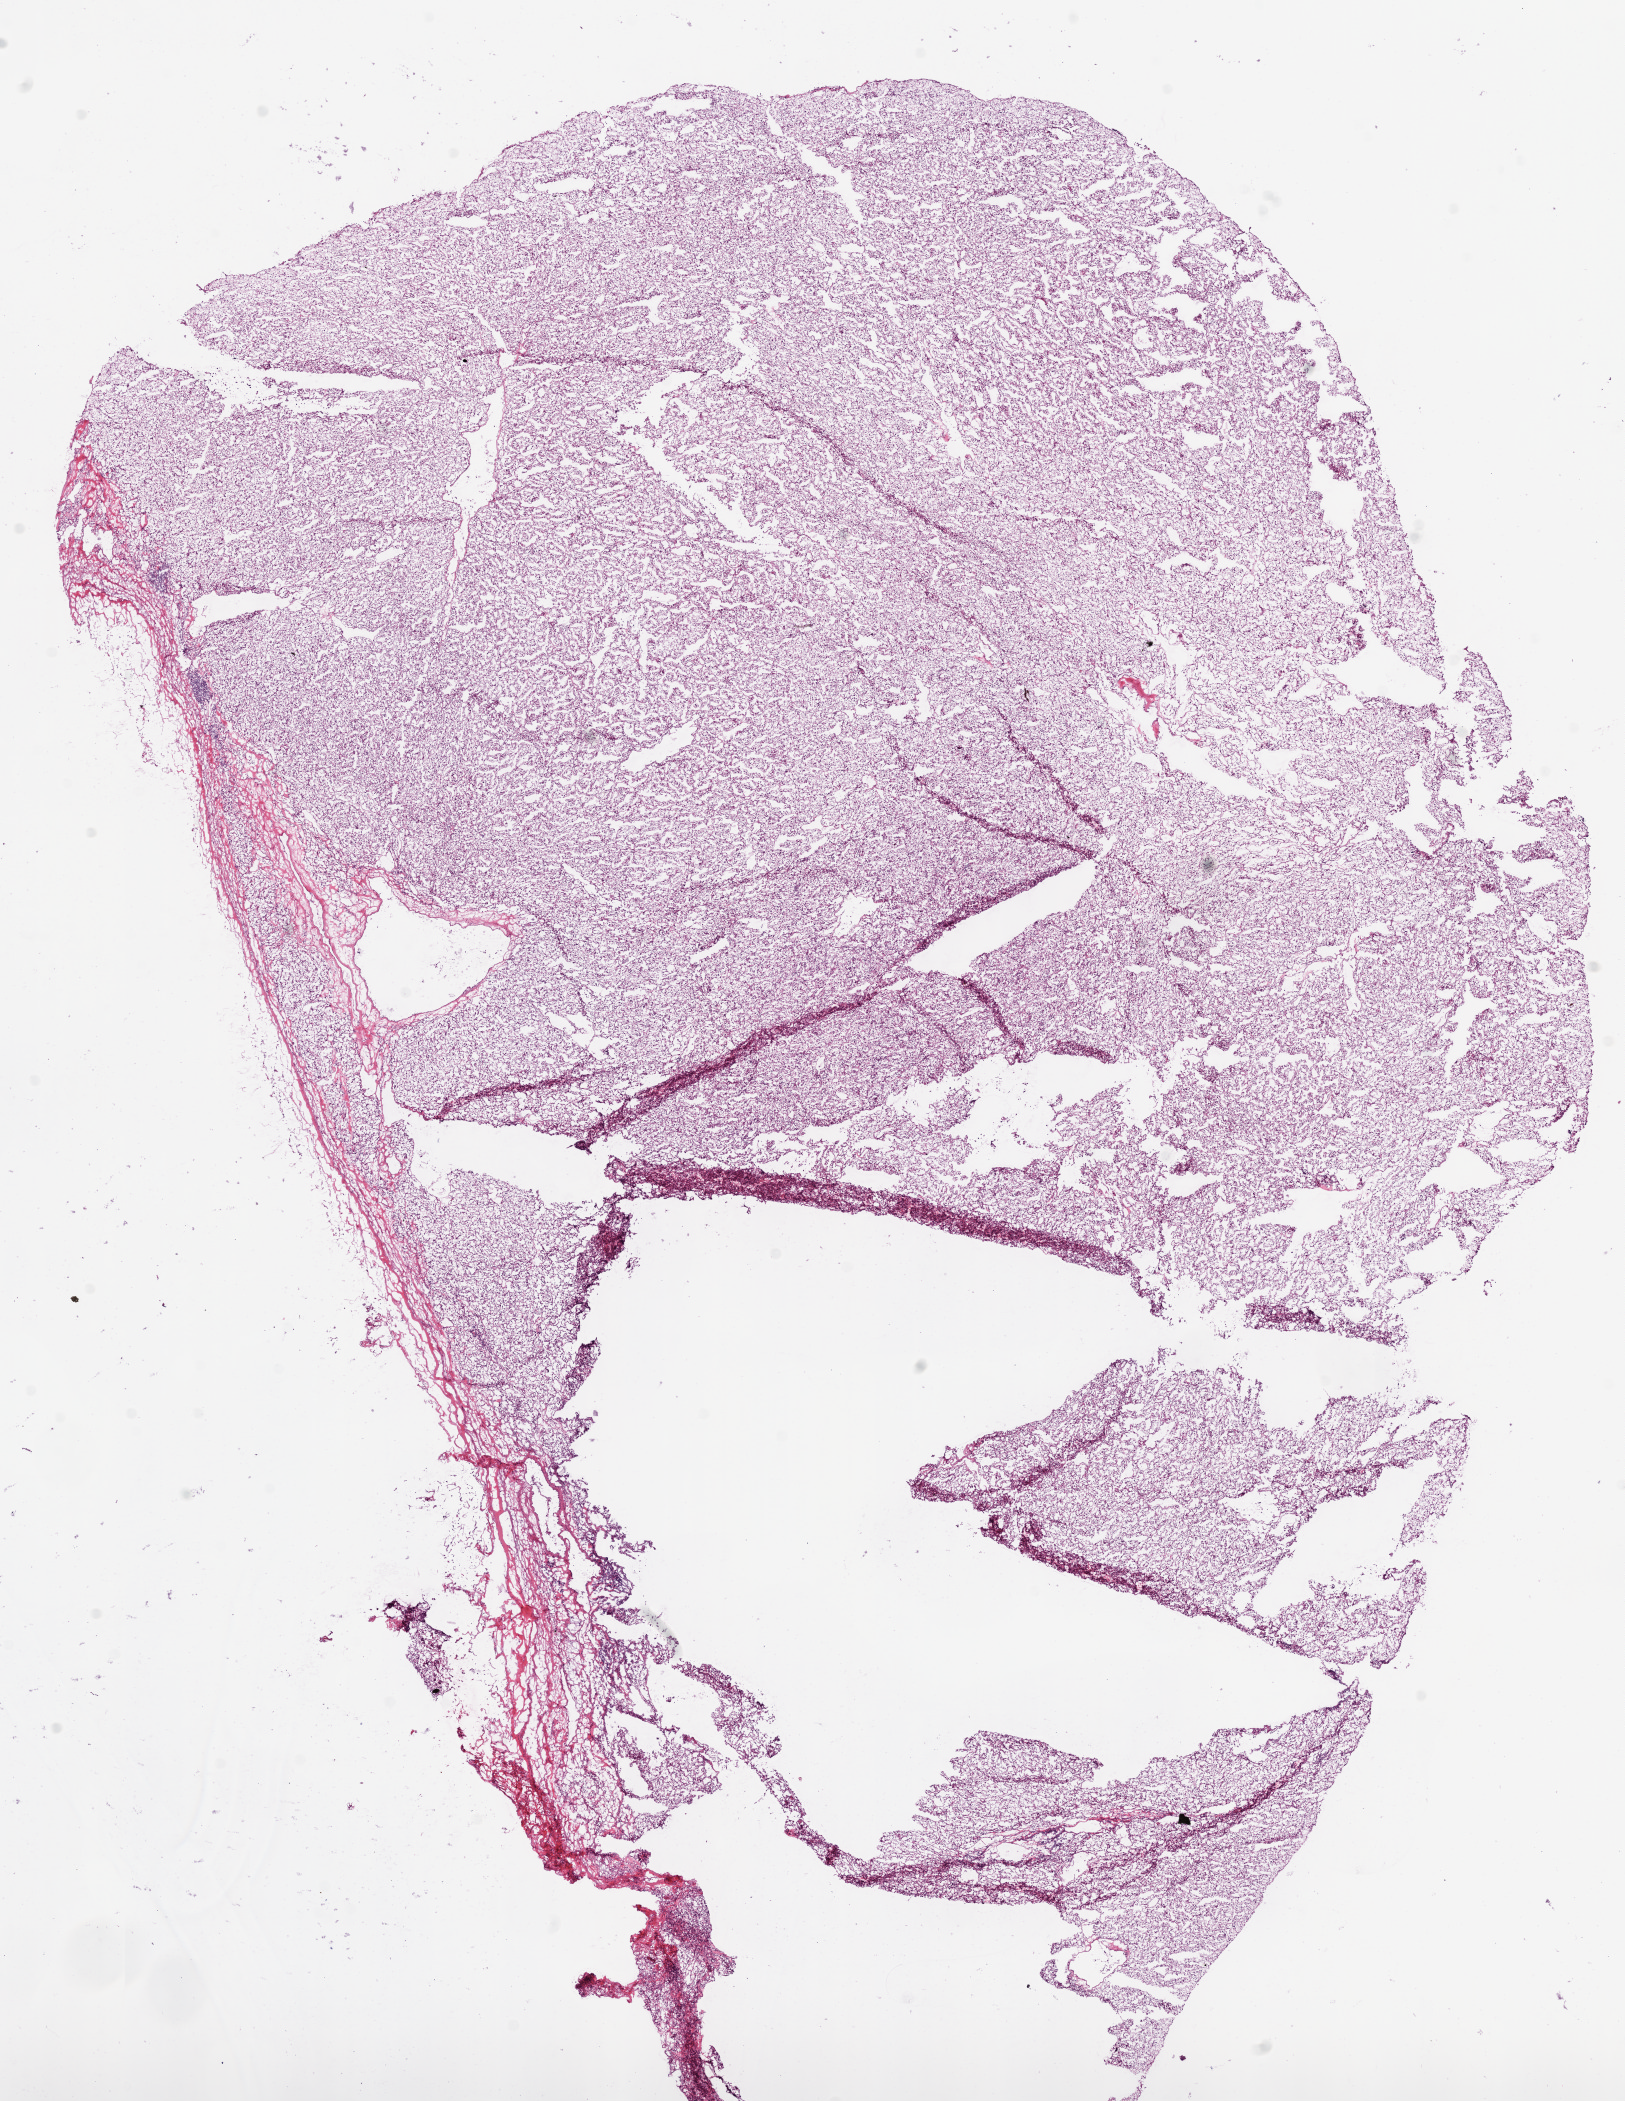
Digitized H&E-stained tissue section (whole slide) — whole scanned area (about 13.0 x 16.9 mm, acquisition: 20x scan) shown as a low-resolution overview, frozen section, sample: primary tumour, kidney. Female, age 65 years at initial diagnosis. Histologic grade: G2 (moderately differentiated). Pathologist review of this section (percent, as recorded): tumour cells 95%, tumour nuclei 90%, normal cells 0%, stromal cells 5%, necrosis 0%.
TNM: T1b N0 M0. Pathologic diagnosis: Clear cell adenocarcinoma, NOS. AJCC pathologic stage: I. Lymph nodes positive (case pathology): 0 of 3 examined.